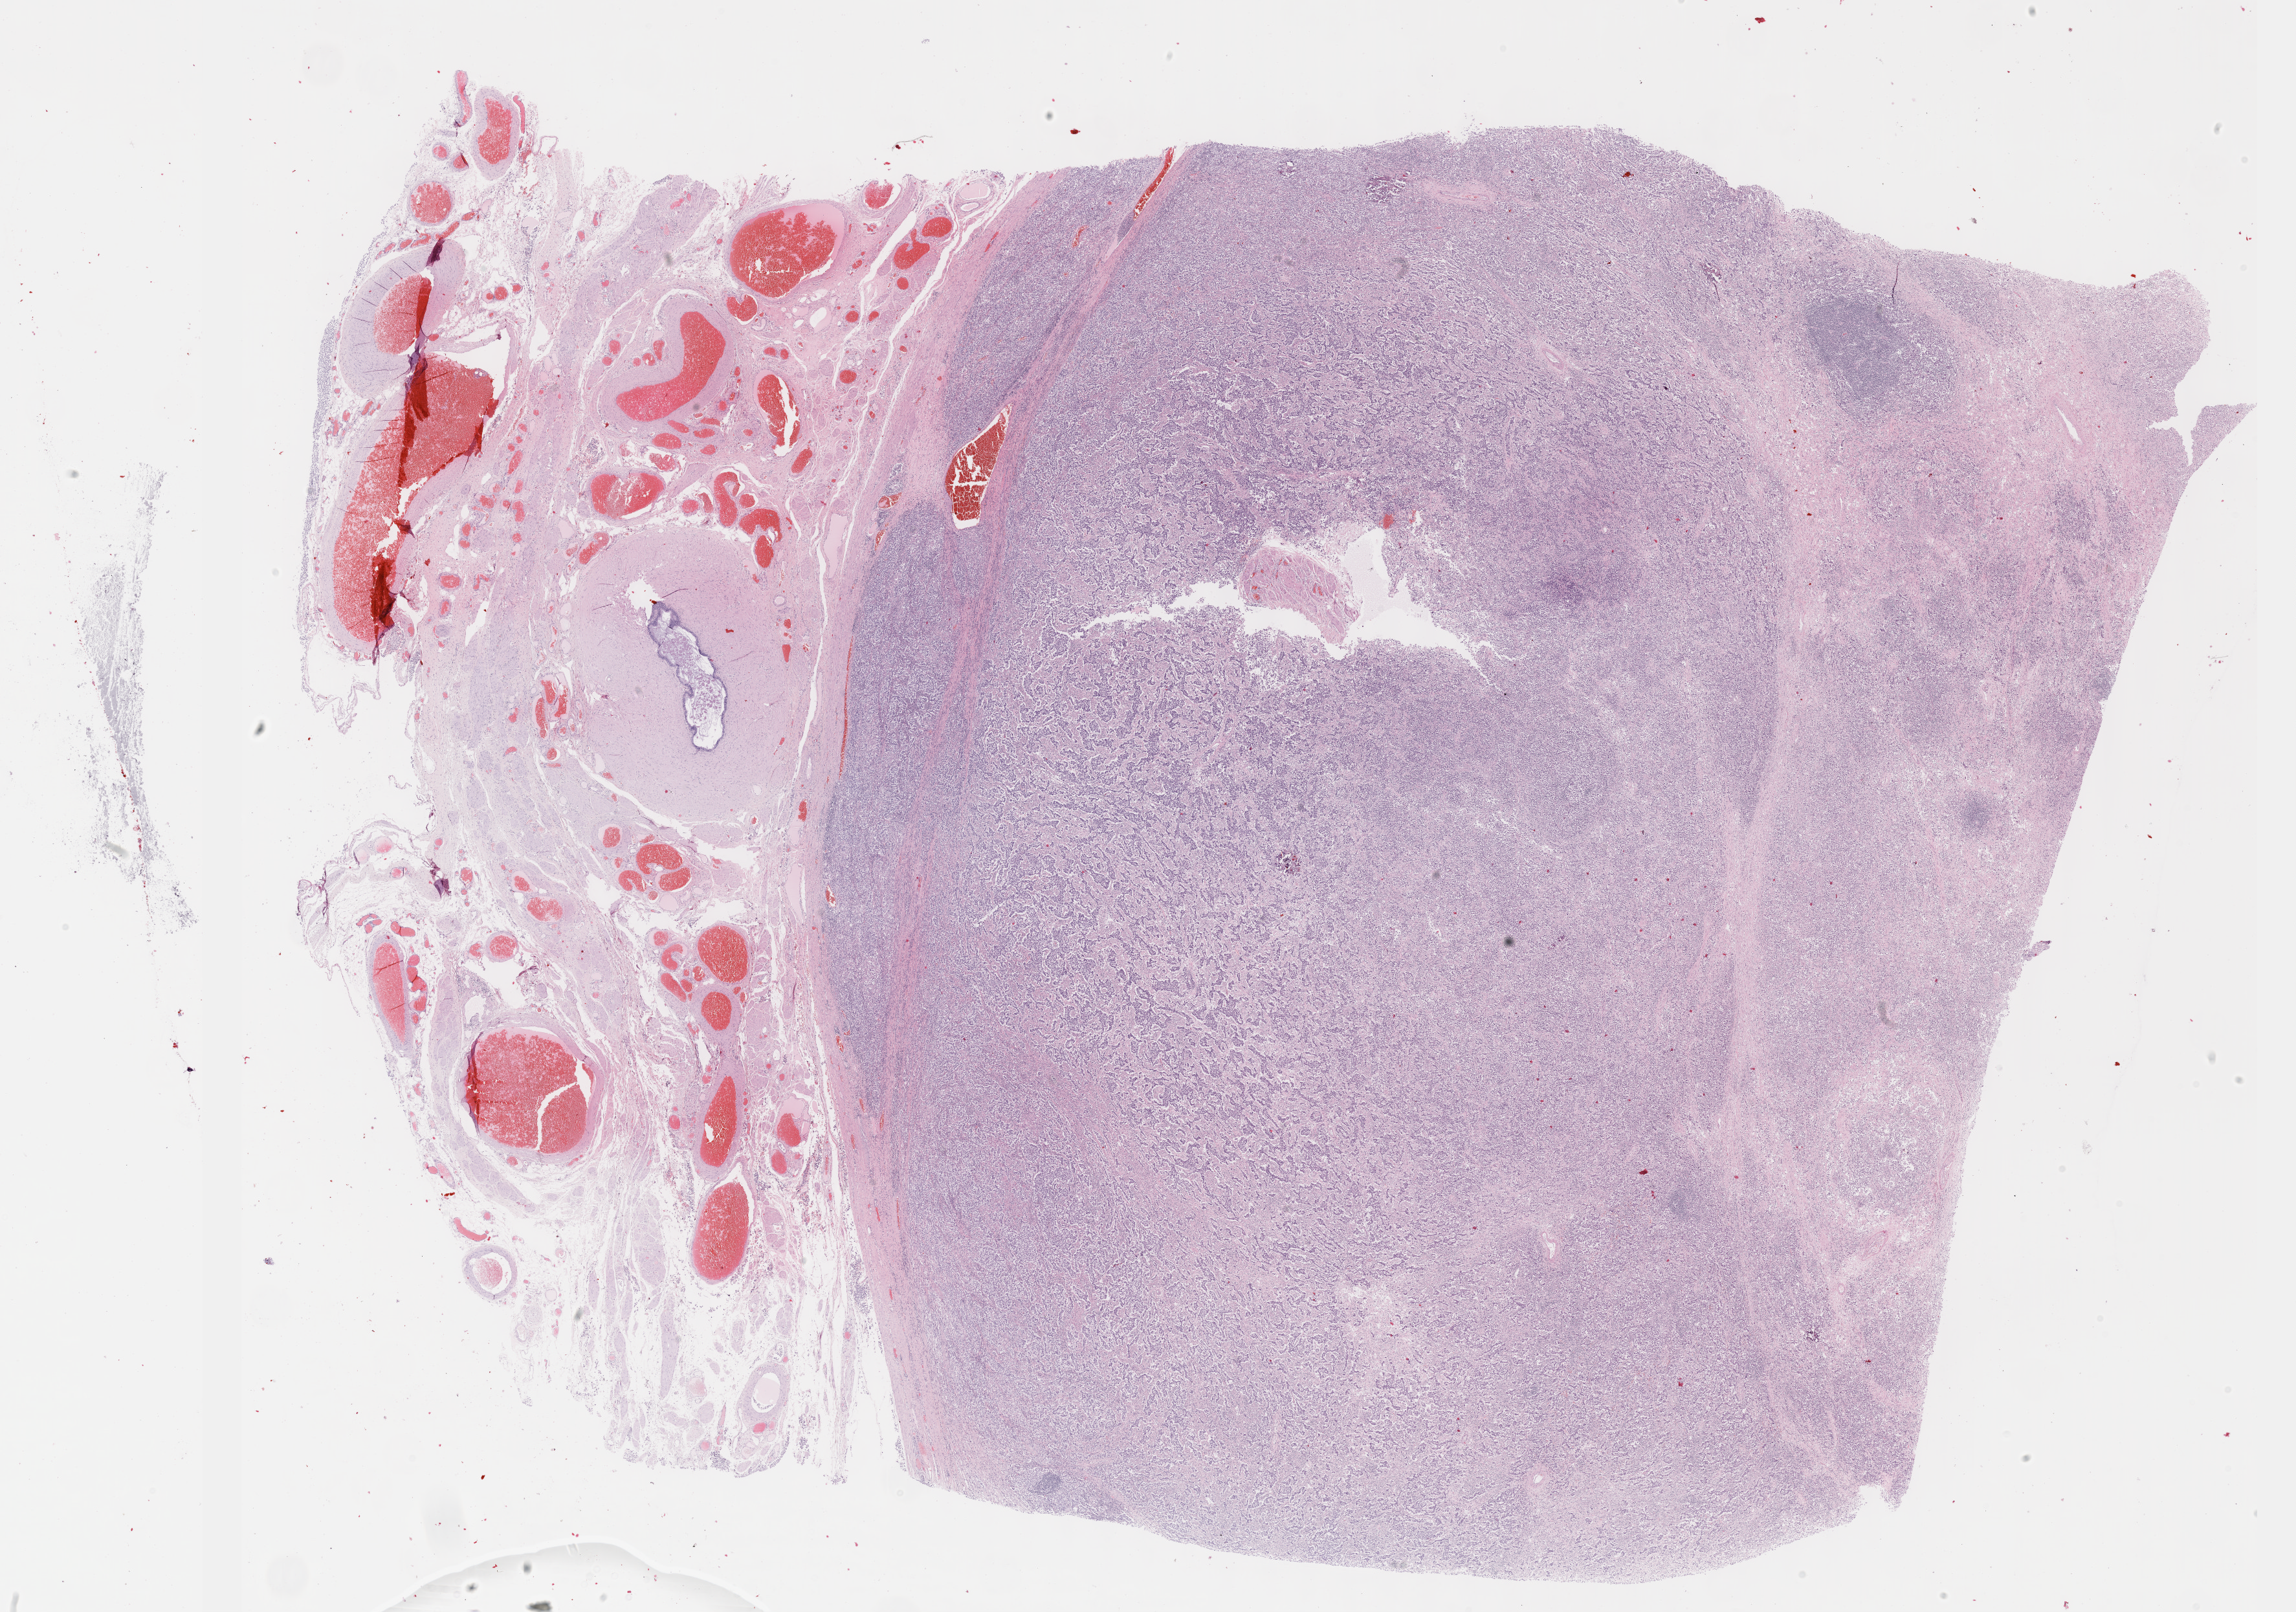
Whole-slide histology image, H&E-stained, low-resolution overview of the scanned area, about 28.7 x 20.1 mm. Formalin-fixed paraffin-embedded (FFPE) diagnostic section. Sample: primary tumour, testis. Male patient; age at initial diagnosis 50 years.
- diagnosis: Seminoma, NOS
- laterality: left
- AJCC pathologic stage: IS